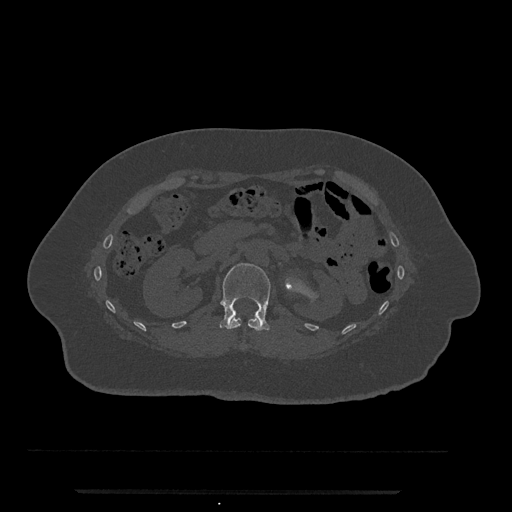
CT including the spine, one axial slice; position 124 of 797 along the scan axis; reconstruction kernel Br40s/3; 120 kVp; bone window (W 1800 / L 400 HU); 0.5 mm slice thickness; 512 × 512 image matrix, field of view 440 × 440 mm. Patient: female, 51 years. Case-level facts recorded for this patient, not image findings: primary cancer: neuro; vertebrae with lytic lesions (as recorded): T8.
Annotated regions visible in this slice (semi-automatic segmentation, software-assisted and operator-edited):
- L1 vertebra: box from (x=219, y=263) to (x=271, y=331) px
- T12 vertebra: (x=227, y=317)–(x=263, y=331)